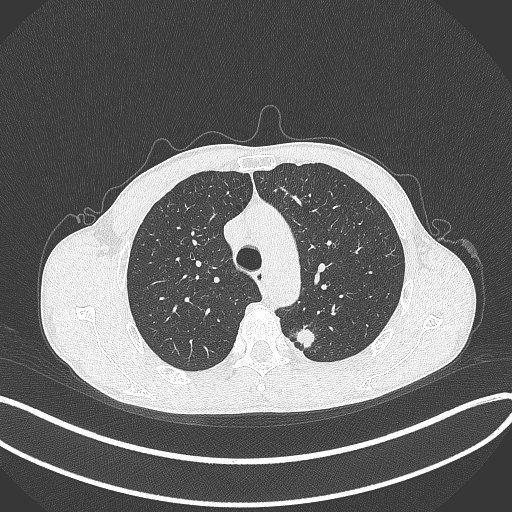
Chest CT, one axial slice; slice 296 of 429 in the series (ordered by position); lung window (W 1500 / L -600 HU); 512 × 512 image matrix. Patient: male, 51 years. From the clinical record (not read from this slice): clinical TNM (as recorded): T2a N1 M1.
Structures marked on this image (rectangle marked by the reading radiologist):
- lung tumour (recorded histology: adenocarcinoma): bounding box [x1, y1, x2, y2] px = [294, 324, 320, 351]